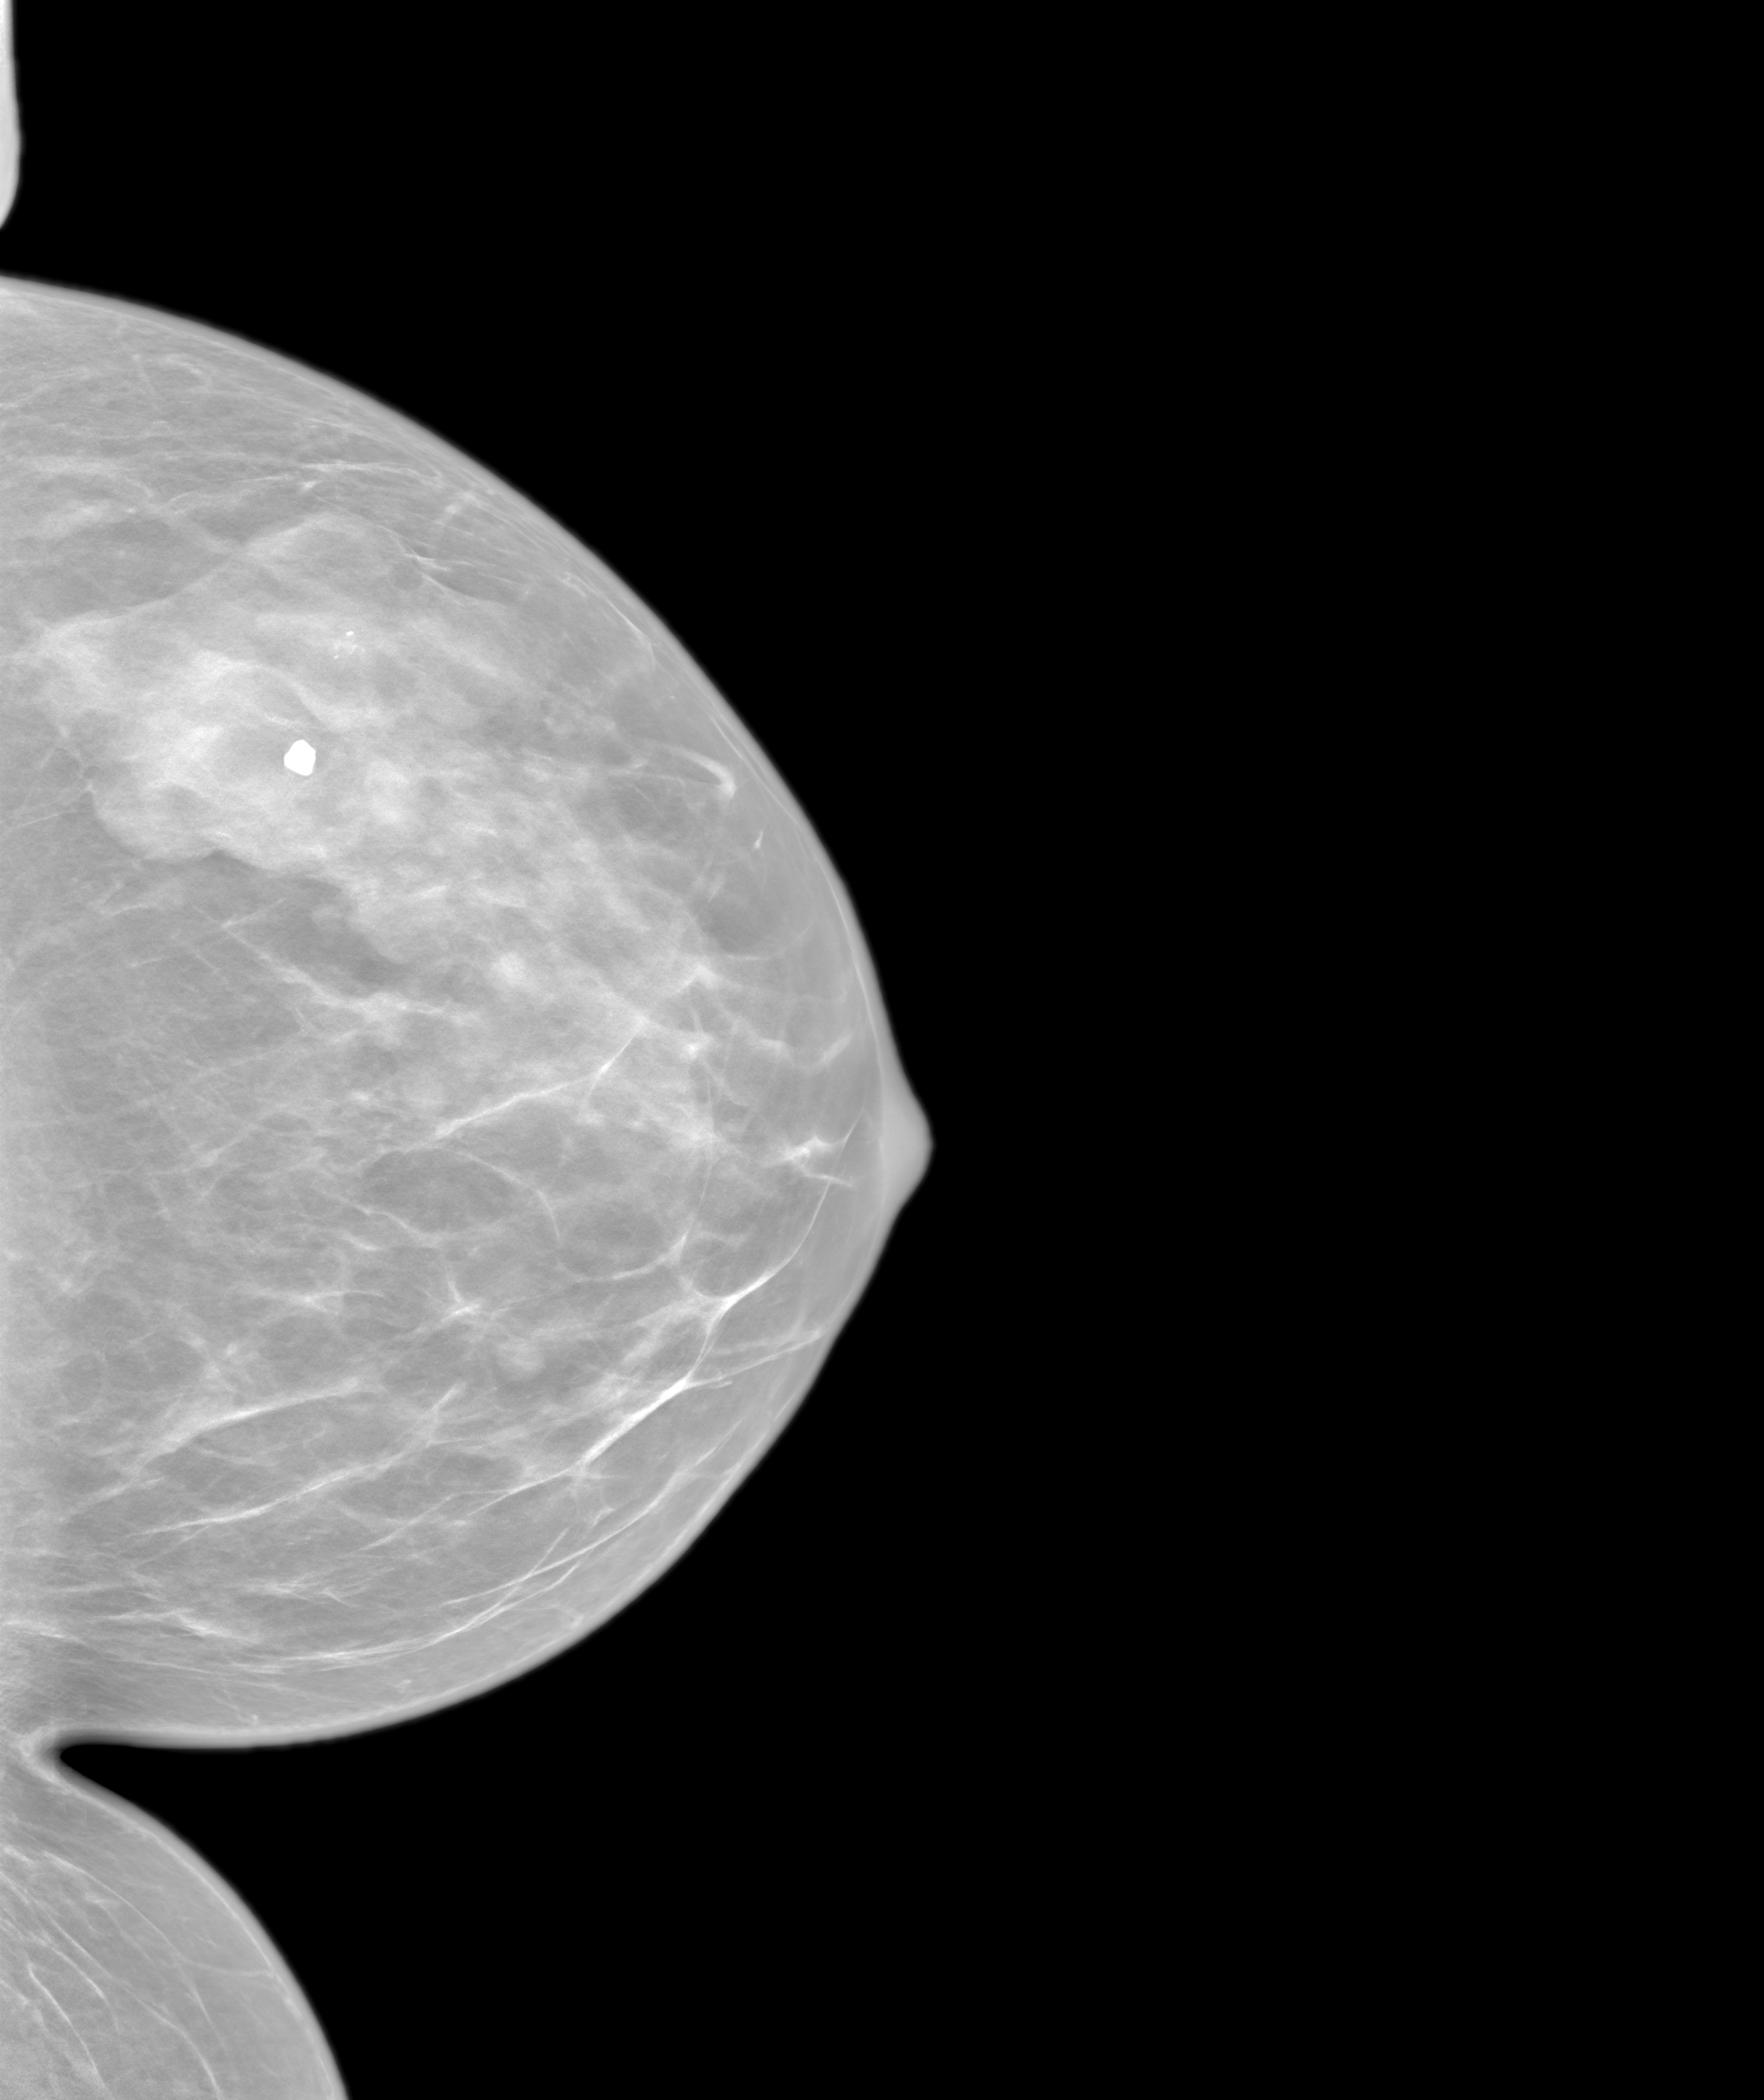
Annual screening mammography examination. Female patient, age 52 years.
Image type: synthesized 2-D view from tomosynthesis. Breast: left. Projection: CC view.